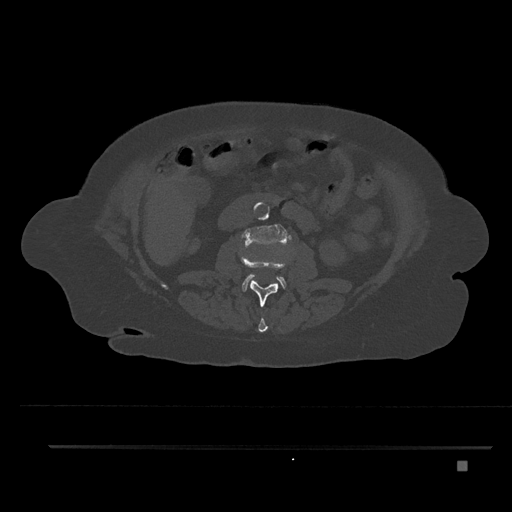
CT including the spine, one axial slice. Slice 164 of 797 in the series (ordered by position). Reconstruction kernel Br40s/3. 120 kVp. Bone window (W 1800 / L 400 HU). 0.5 mm slice thickness. 512 × 512 image matrix, field of view 437 × 437 mm. Patient: female, 76 years. Case-level facts recorded for this patient, not image findings: primary cancer: lung; vertebrae with lytic lesions (as recorded): T11, L3.
Outlined on this slice (semi-automatic segmentation, software-assisted and operator-edited):
- L1 vertebra: bounding box (x1, y1, x2, y2) in pixels: (258, 317, 268, 333)
- L2 vertebra: (241, 256, 287, 307)
- L3 vertebra: (241, 224, 291, 292)